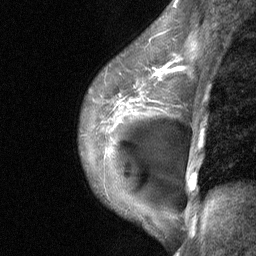
Breast MRI (dynamic contrast-enhanced), one sagittal slice; position 47 of 64 along the scan axis; dynamic contrast-enhanced study with each time point stored as its own series, time point 2 of 3 at this slice position (early post-contrast, ordered by acquisition time); 1.5 T; TE 4.8 ms, TR 27 ms; 2 mm slice thickness; 256 × 256 image matrix. Patient: female, 35 years. From the clinical record (not read from this slice): setting: breast cancer imaged before/during neoadjuvant chemotherapy; receptor status: HR-positive, HER2-negative.
Annotated regions visible in this slice (semi-automatically segmented with operator editing):
- analysis volume of interest (the breast-tissue region the enhancement analysis was run in; not a lesion): bounding box [x1, y1, x2, y2] px = [79, 58, 187, 171]
- tumour enhancement mask (voxels above the 90 % enhancement threshold inside the analysis volume of interest): [130, 66, 180, 100]